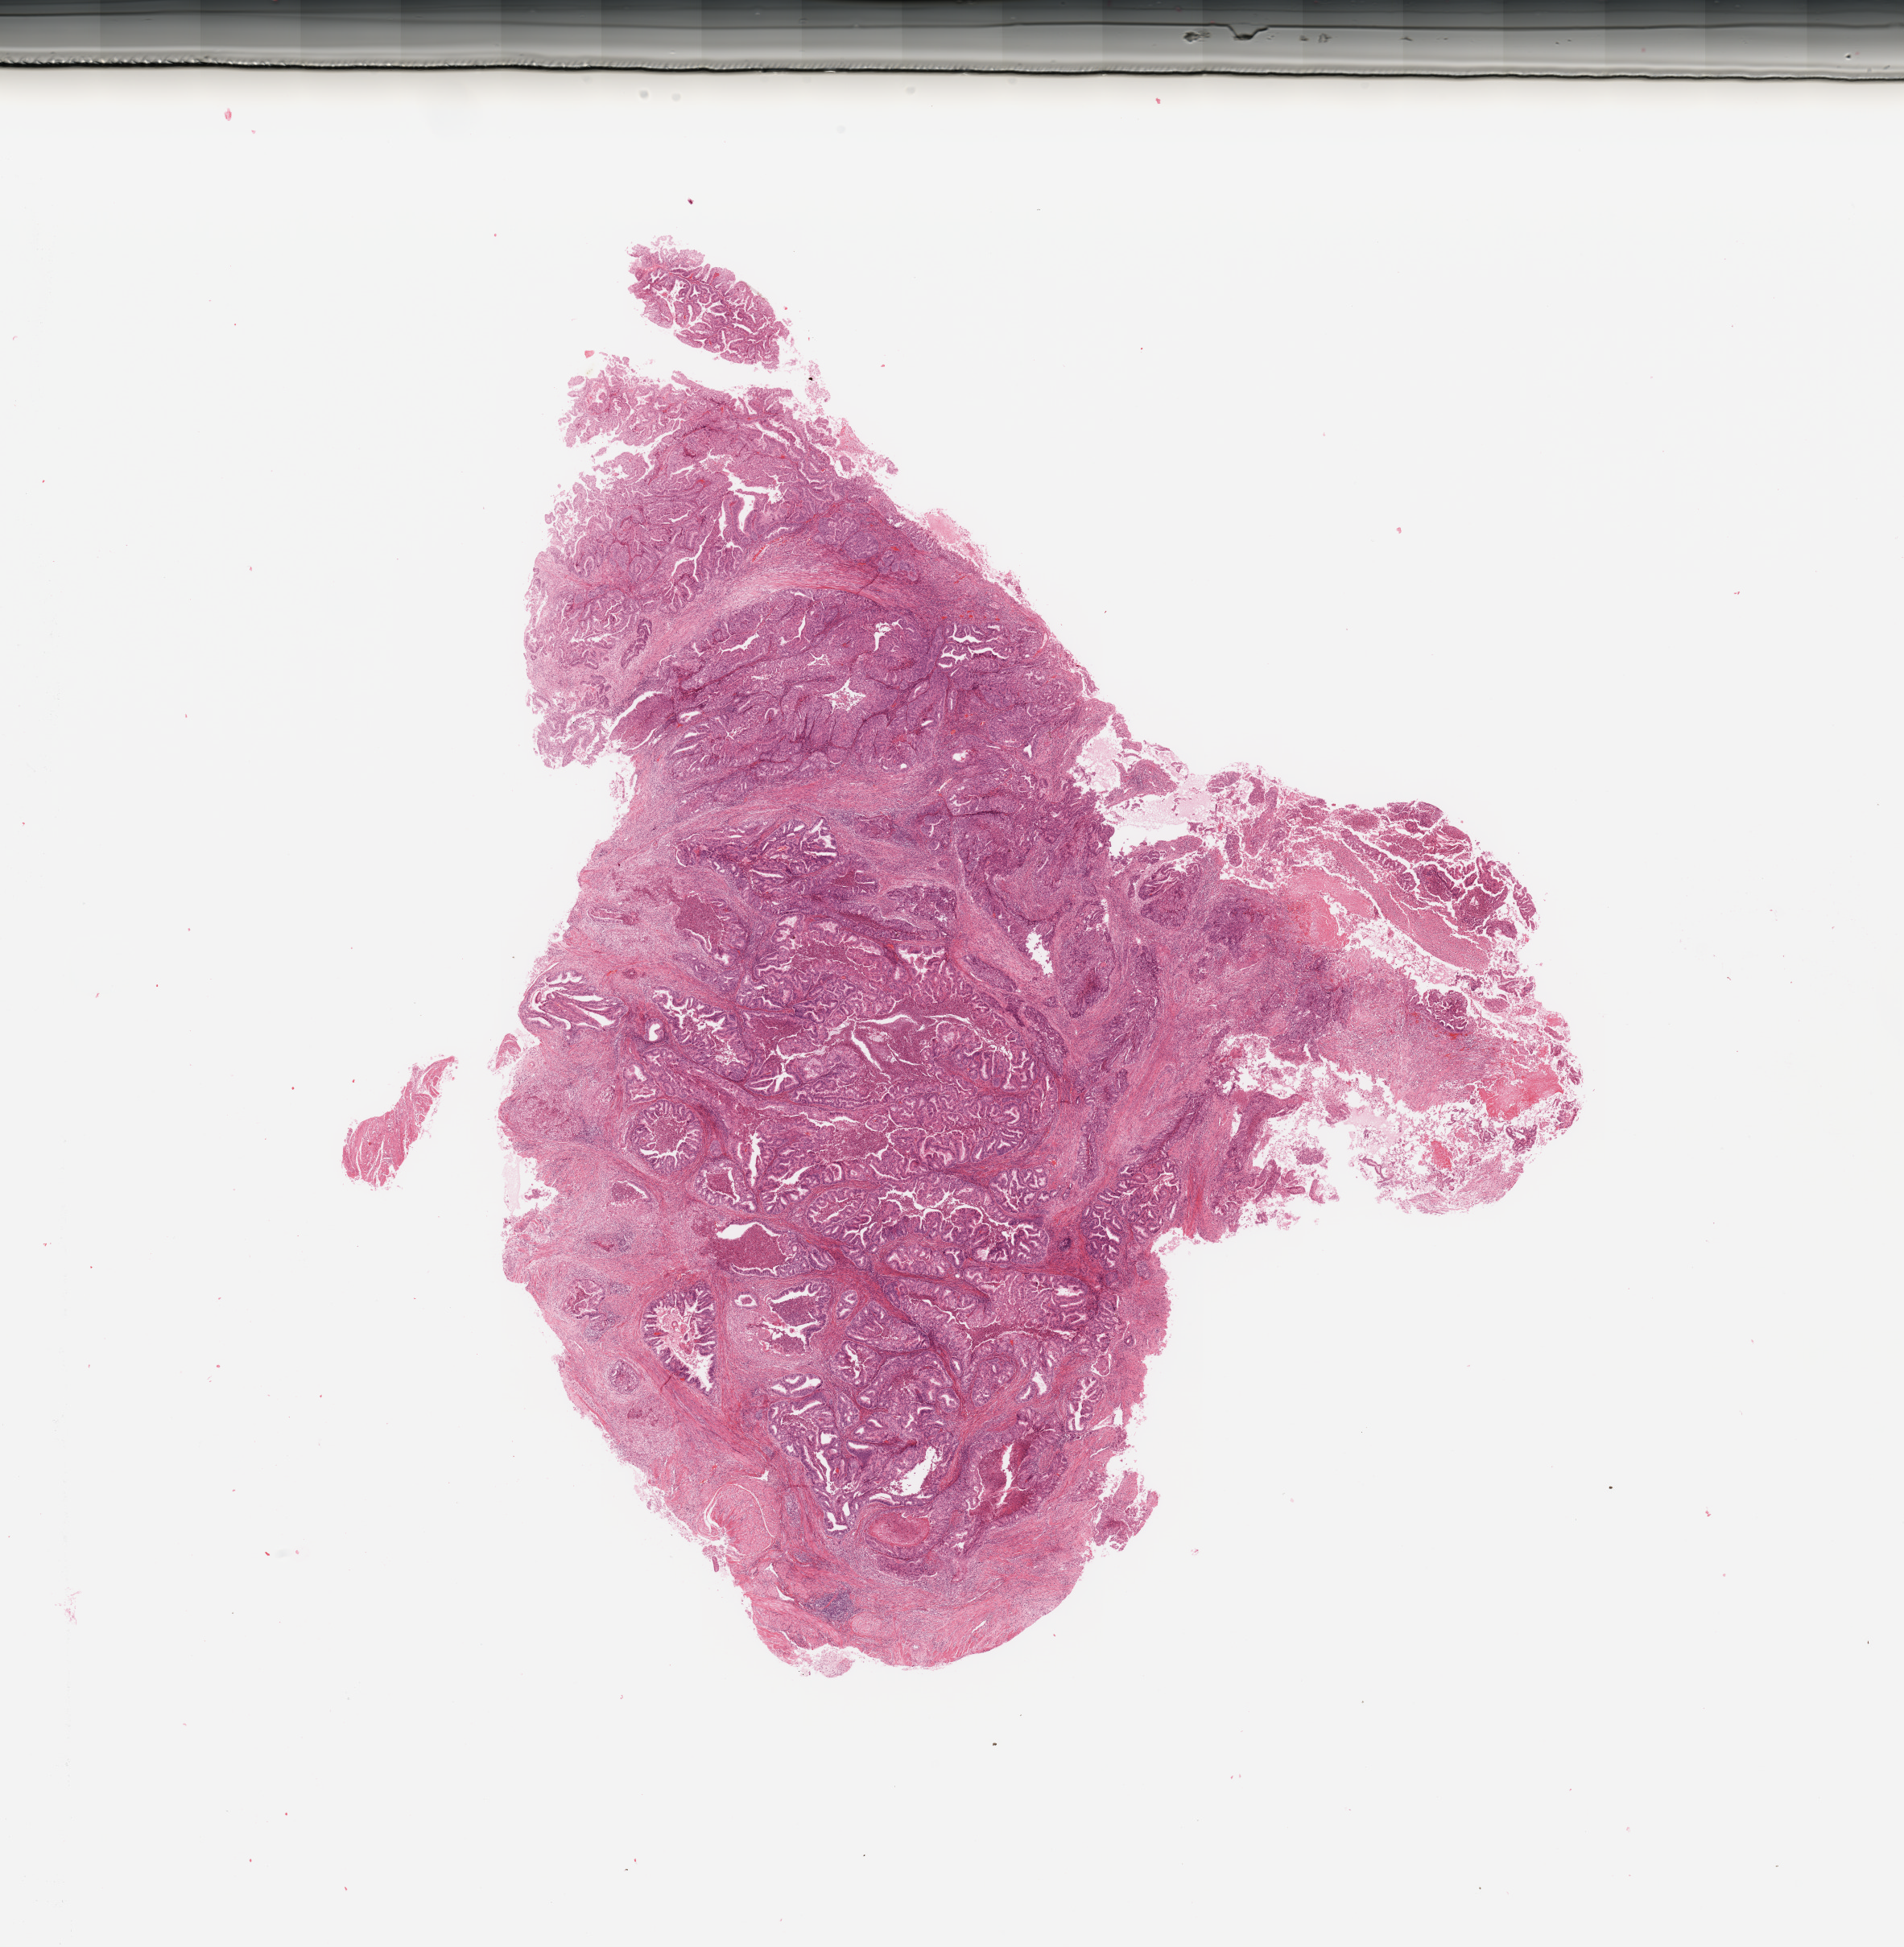
H&E whole-slide image — shown as a low-resolution overview of the whole scanned area (about 18.7 x 19.1 mm); tumour tissue sample, uterus. Patient: female, age 60 years. Histologic grade: G3 (poorly differentiated).
AJCC pathologic stage: I. Diagnosis: Endometrioid adenocarcinoma, NOS.